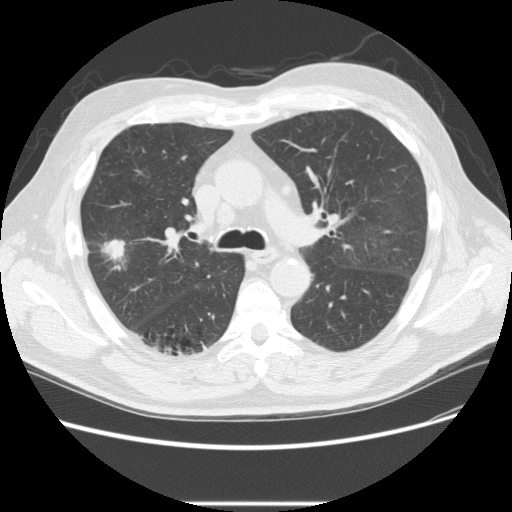
Low-dose screening chest CT, one axial slice. Slice 147 of 233 in the series (ordered by position). Reconstruction kernel STANDARD. 120 kVp. Lung window (W 1500 / L -600 HU). 512 × 512 image matrix, field of view 380 × 380 mm.
Structures marked on this image (manually delineated by an expert):
- lesion 2 (tumor, upper lobe of right lung): bounding box (x1, y1, x2, y2) in pixels: (102, 239, 125, 260)